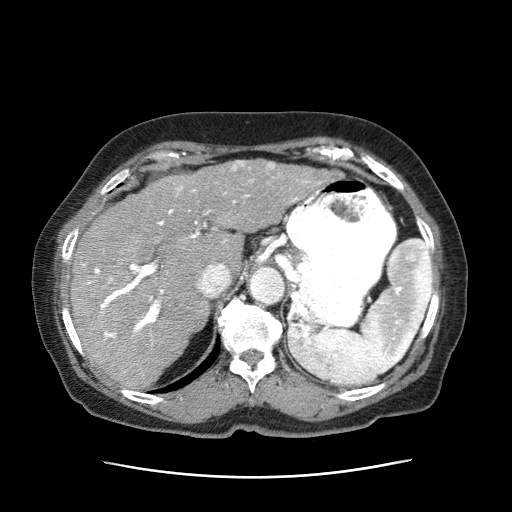
Contrast-enhanced abdominal CT (liver protocol), one axial slice; position 46 of 63 along the scan axis; intravenous contrast given; soft-tissue window (W 400 / L 40 HU); 2.5 mm slice thickness; 512 × 512 image matrix, field of view 360 × 360 mm. Patient: female, 79 years. From the clinical record (not read from this slice): diagnosis: hepatocellular carcinoma (patient treated with transarterial chemoembolisation; whether this scan precedes or follows treatment is not stated here); TNM stage (as recorded): Stage-II; Child-Pugh class: B; tumour differentiation: well differentiated.
Annotated regions visible in this slice (semi-automatic segmentation, software-assisted and operator-edited):
- abdominal aorta: bounding box (x1, y1, x2, y2) in pixels: (249, 269, 286, 306)
- liver parenchyma outside the tumour (the mass and vessels are separate outlines, so this box may not span the whole liver): (70, 172, 247, 391)
- mass: (192, 160, 340, 233)
- liver vessels: (85, 178, 299, 342)